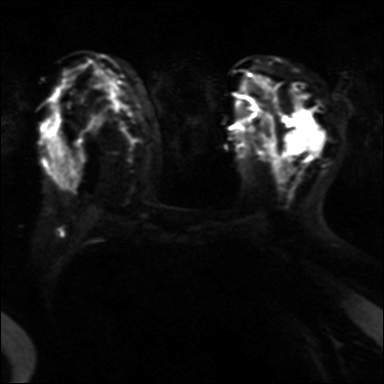
Breast MRI, one axial slice. Slice 19 of 40 in the series (ordered by position). Diffusion-weighted series; image 2 of 4 stored at this slice position (different b-values; order by instance number). 3 T. 4 mm slice thickness. 384 × 384 image matrix, field of view 320 × 320 mm. Female patient.
Outlined on this slice (manually delineated by an expert):
- tumour on diffusion-weighted imaging: bounding box [x1, y1, x2, y2] px = [290, 117, 316, 152]